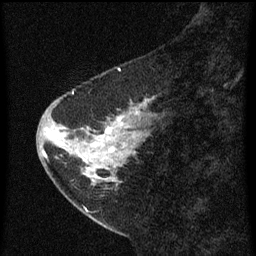
Breast MRI (dynamic contrast-enhanced), one sagittal slice; position 20 of 60 along the scan axis; dynamic contrast-enhanced series, image 2 of 3 at this slice position (ordered by acquisition); 1.5 T; TE 4.2 ms, TR 8 ms; 2 mm slice thickness; 256 × 256 image matrix, field of view 180 × 180 mm. Patient: female, 47 years.
Structures marked on this image (semi-automatic segmentation, software-assisted and operator-edited):
- analysis volume of interest (the breast-tissue region the enhancement analysis was run in; not a lesion): bounding box (x1, y1, x2, y2) in pixels: (44, 90, 155, 199)
- tumour enhancement mask (voxels above the 70 % enhancement threshold inside the analysis volume of interest): (44, 92, 147, 185)